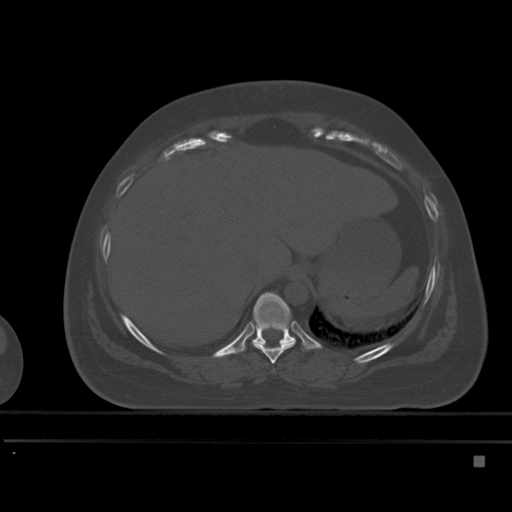
CT including the spine, one axial slice; slice 256 of 495 in the series (ordered by position); bone window (W 1800 / L 400 HU); 1.5 mm slice thickness; 512 × 512 image matrix. Female patient, age 33 years. Case-level facts recorded for this patient, not image findings: primary cancer: breast.
Annotated regions visible in this slice (semi-automatic segmentation, software-assisted and operator-edited):
- T10 vertebra: bounding box (x1, y1, x2, y2) in pixels: (240, 292, 296, 352)
- T9 vertebra: (252, 340, 296, 364)